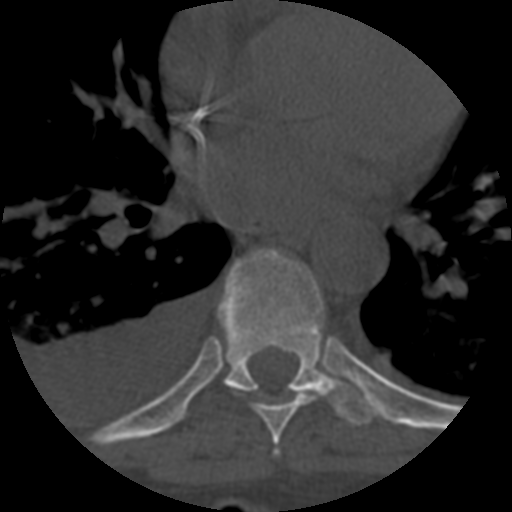
CT including the spine, one axial slice; slice 405 of 708 in the series (ordered by position); reconstruction kernel STANDARD; one of 3 acquisitions stored at this slice position; bone window (W 1800 / L 400 HU); 1.25 mm slice thickness; 512 × 512 image matrix, field of view 160 × 160 mm. Patient age 55 years. Case-level facts recorded for this patient, not image findings: primary cancer: colon.
Outlined on this slice (semi-automatically segmented with operator editing):
- T7 vertebra: bounding box (x1, y1, x2, y2) in pixels: (253, 389, 320, 447)
- T8 vertebra: (217, 250, 375, 426)